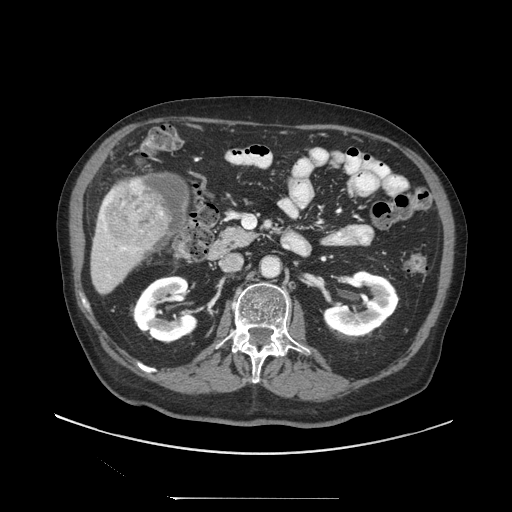
Contrast-enhanced abdominal CT (liver protocol), one axial slice. Slice 36 of 97 in the series (ordered by position). Soft-tissue window (W 400 / L 40 HU). 2.5 mm slice thickness. 512 × 512 image matrix, field of view 450 × 450 mm. Case-level facts recorded for this patient, not image findings: diagnosis: hepatocellular carcinoma (patient treated with transarterial chemoembolisation; whether this scan precedes or follows treatment is not stated here); TNM stage (as recorded): Stage-IIIC; Child-Pugh class: A; tumour differentiation: well differentiated; tumour size: 9.2 cm.
Structures marked on this image (semi-automatic segmentation, software-assisted and operator-edited):
- liver parenchyma outside the tumour (the mass and vessels are separate outlines, so this box may not span the whole liver): bounding box (x1, y1, x2, y2) in pixels: (90, 176, 170, 294)
- mass: (106, 182, 168, 246)
- liver vessels: (100, 192, 127, 250)